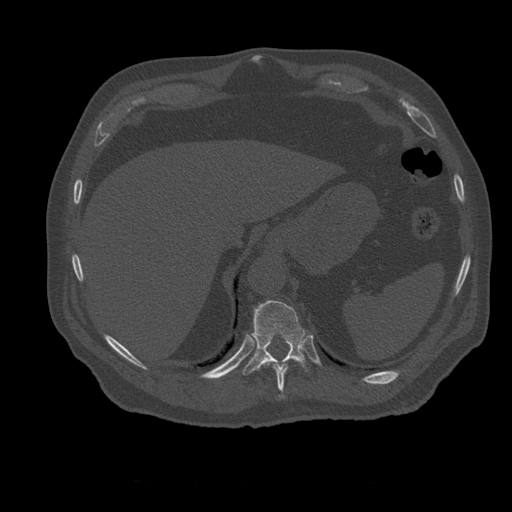
CT including the spine, one axial slice; slice 287 of 399 in the series (ordered by position); reconstruction kernel STANDARD; bone window (W 1800 / L 400 HU); 1.25 mm slice thickness; 512 × 512 image matrix, field of view 407 × 407 mm. Patient age 73 years. Case-level facts recorded for this patient, not image findings: primary cancer: prostate; vertebrae with lytic lesions (as recorded): L2.
Structures marked on this image (semi-automatic segmentation, software-assisted and operator-edited):
- T10 vertebra: bounding box (x1, y1, x2, y2) in pixels: (267, 361, 300, 398)
- T11 vertebra: (243, 300, 313, 376)